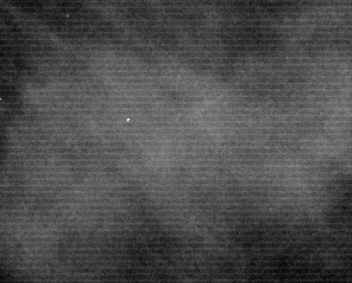
Region of interest cut from a scanned film mammogram (one marked finding); right breast; CC view.
Mass, shape round, margins circumscribed; BI-RADS assessment category 2; pathology result (as recorded, not read from the image): benign.